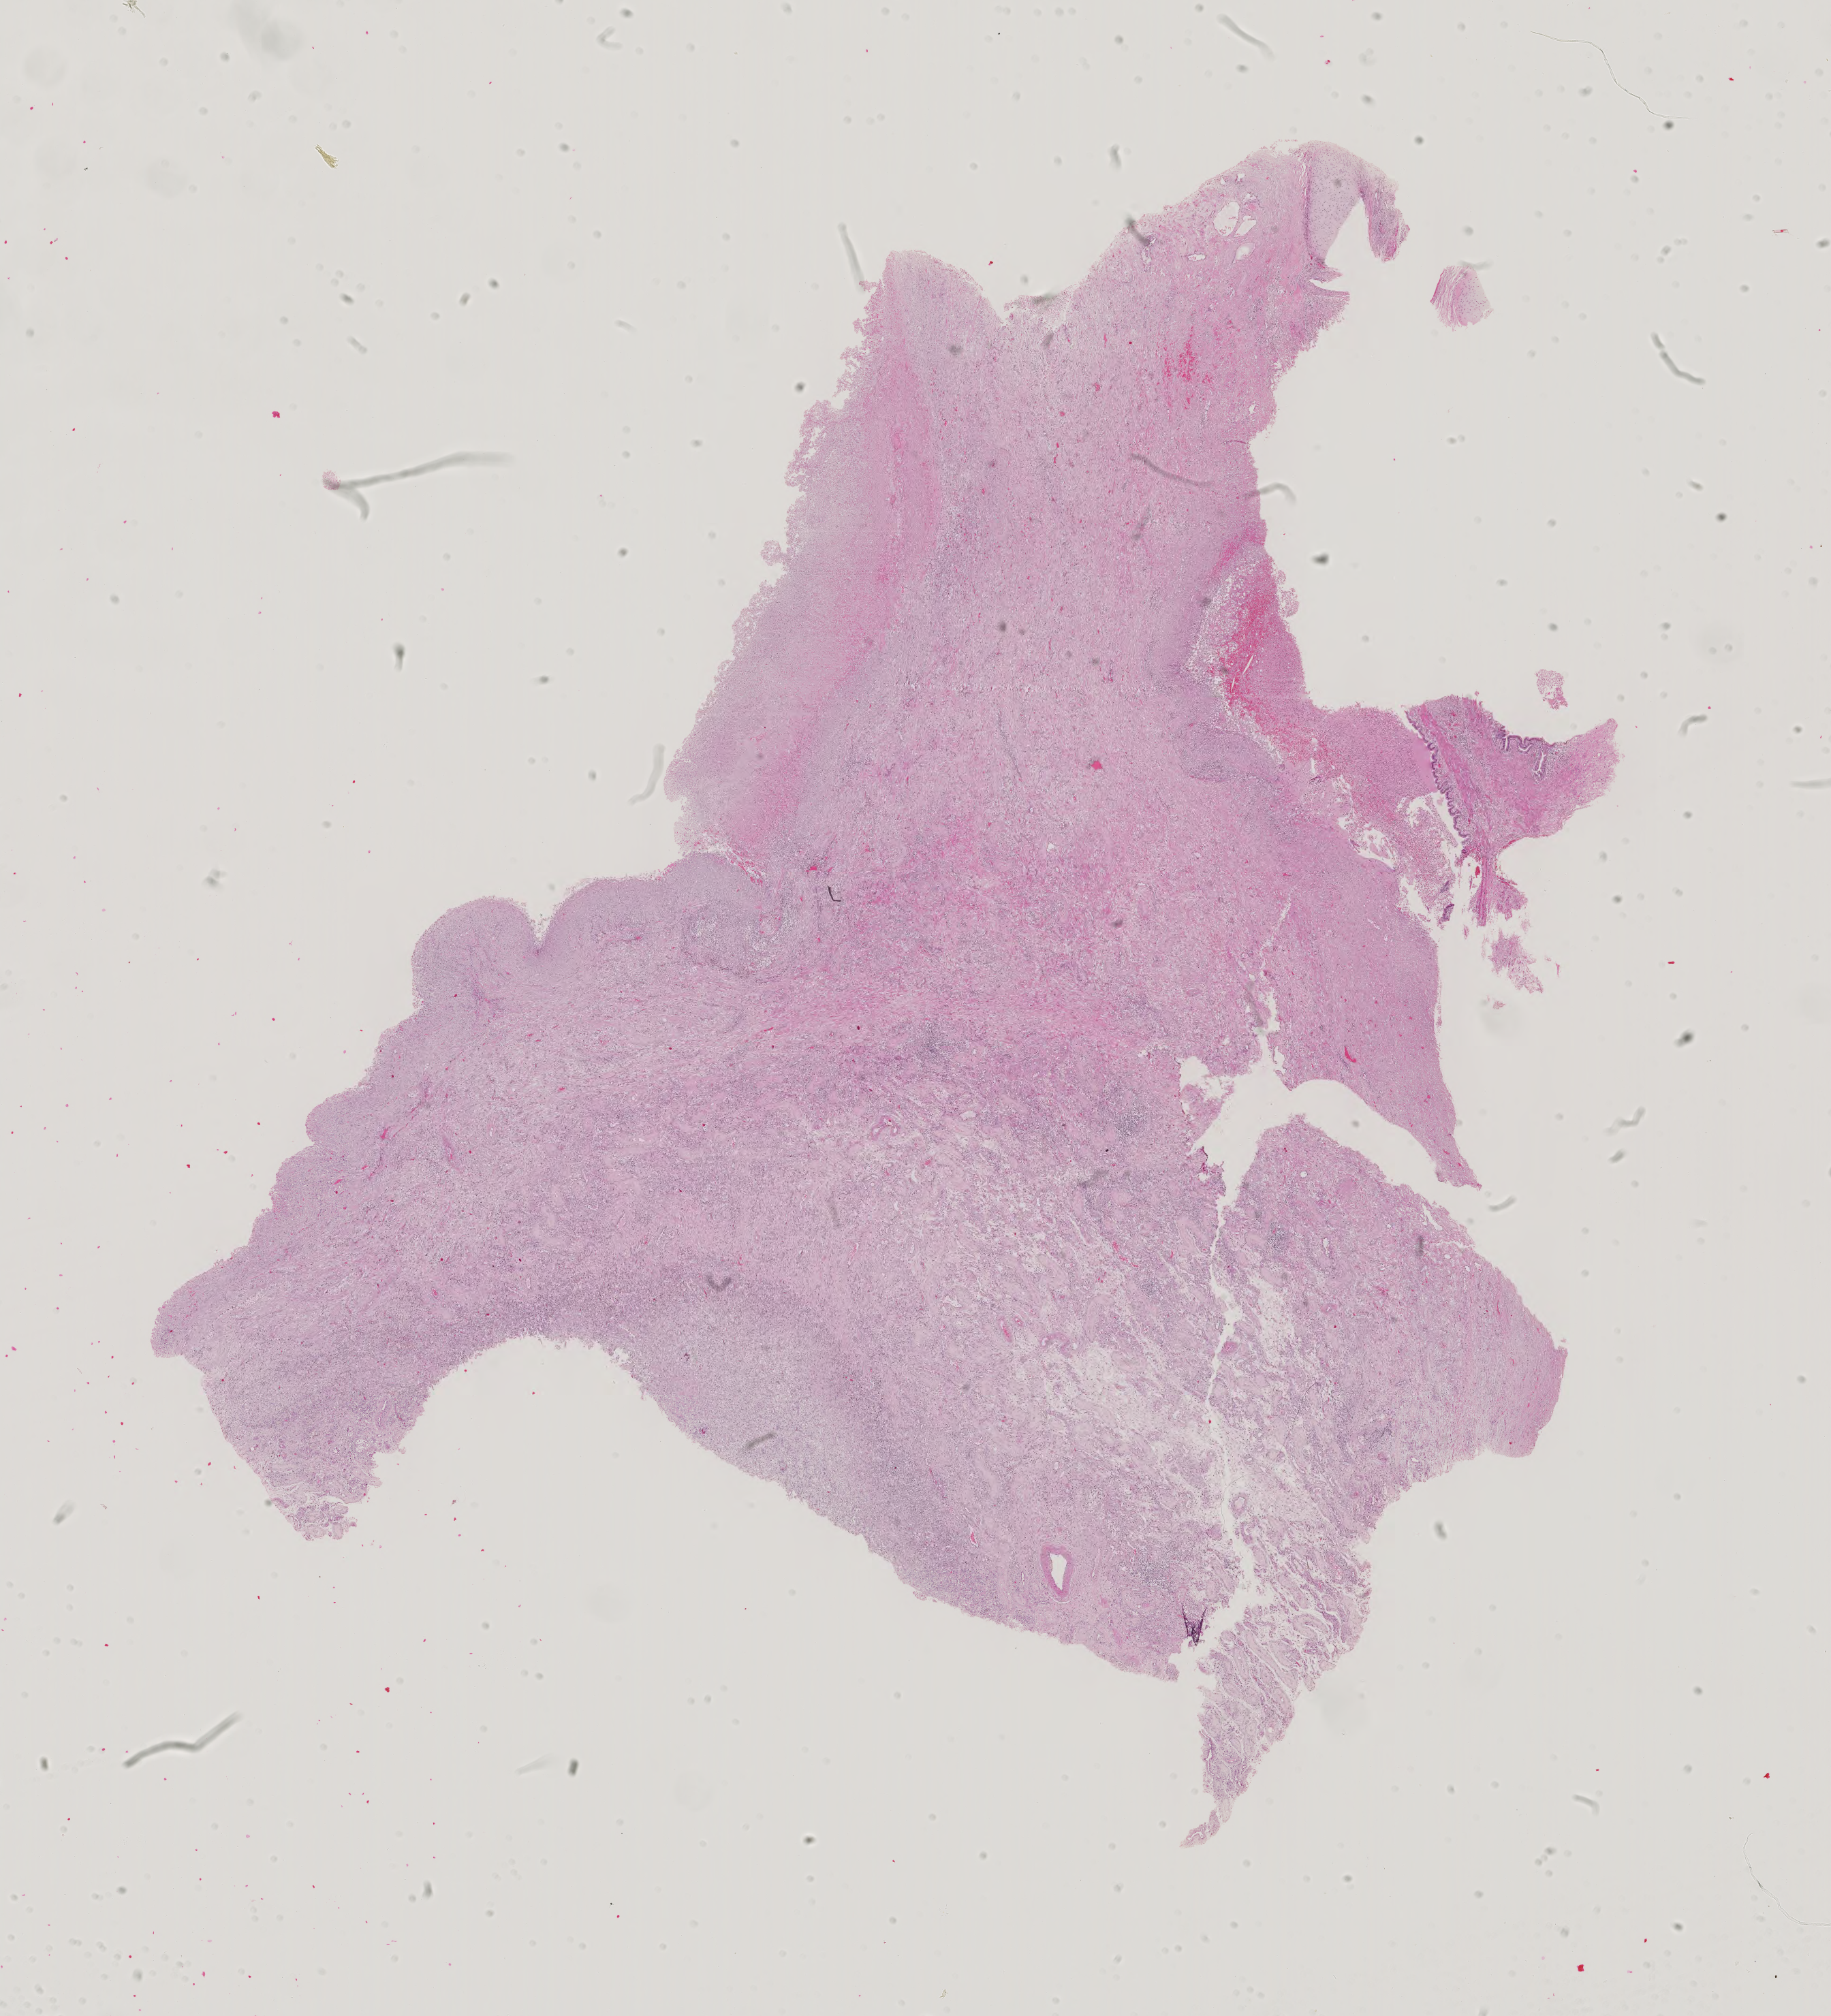
Digitized Hematoxylin and eosin (H&E) stained tissue section (whole slide) — low-resolution overview of the scanned area, about 19.6 x 21.6 mm. Formalin-fixed paraffin-embedded (FFPE) diagnostic section. Testis, primary tumour sample. Patient: male, age at initial diagnosis 43 years.
TNM: T1 NX M1. Laterality: left. AJCC pathologic stage: IIIB (6th edition). Pathologic diagnosis: Mixed germ cell tumor.